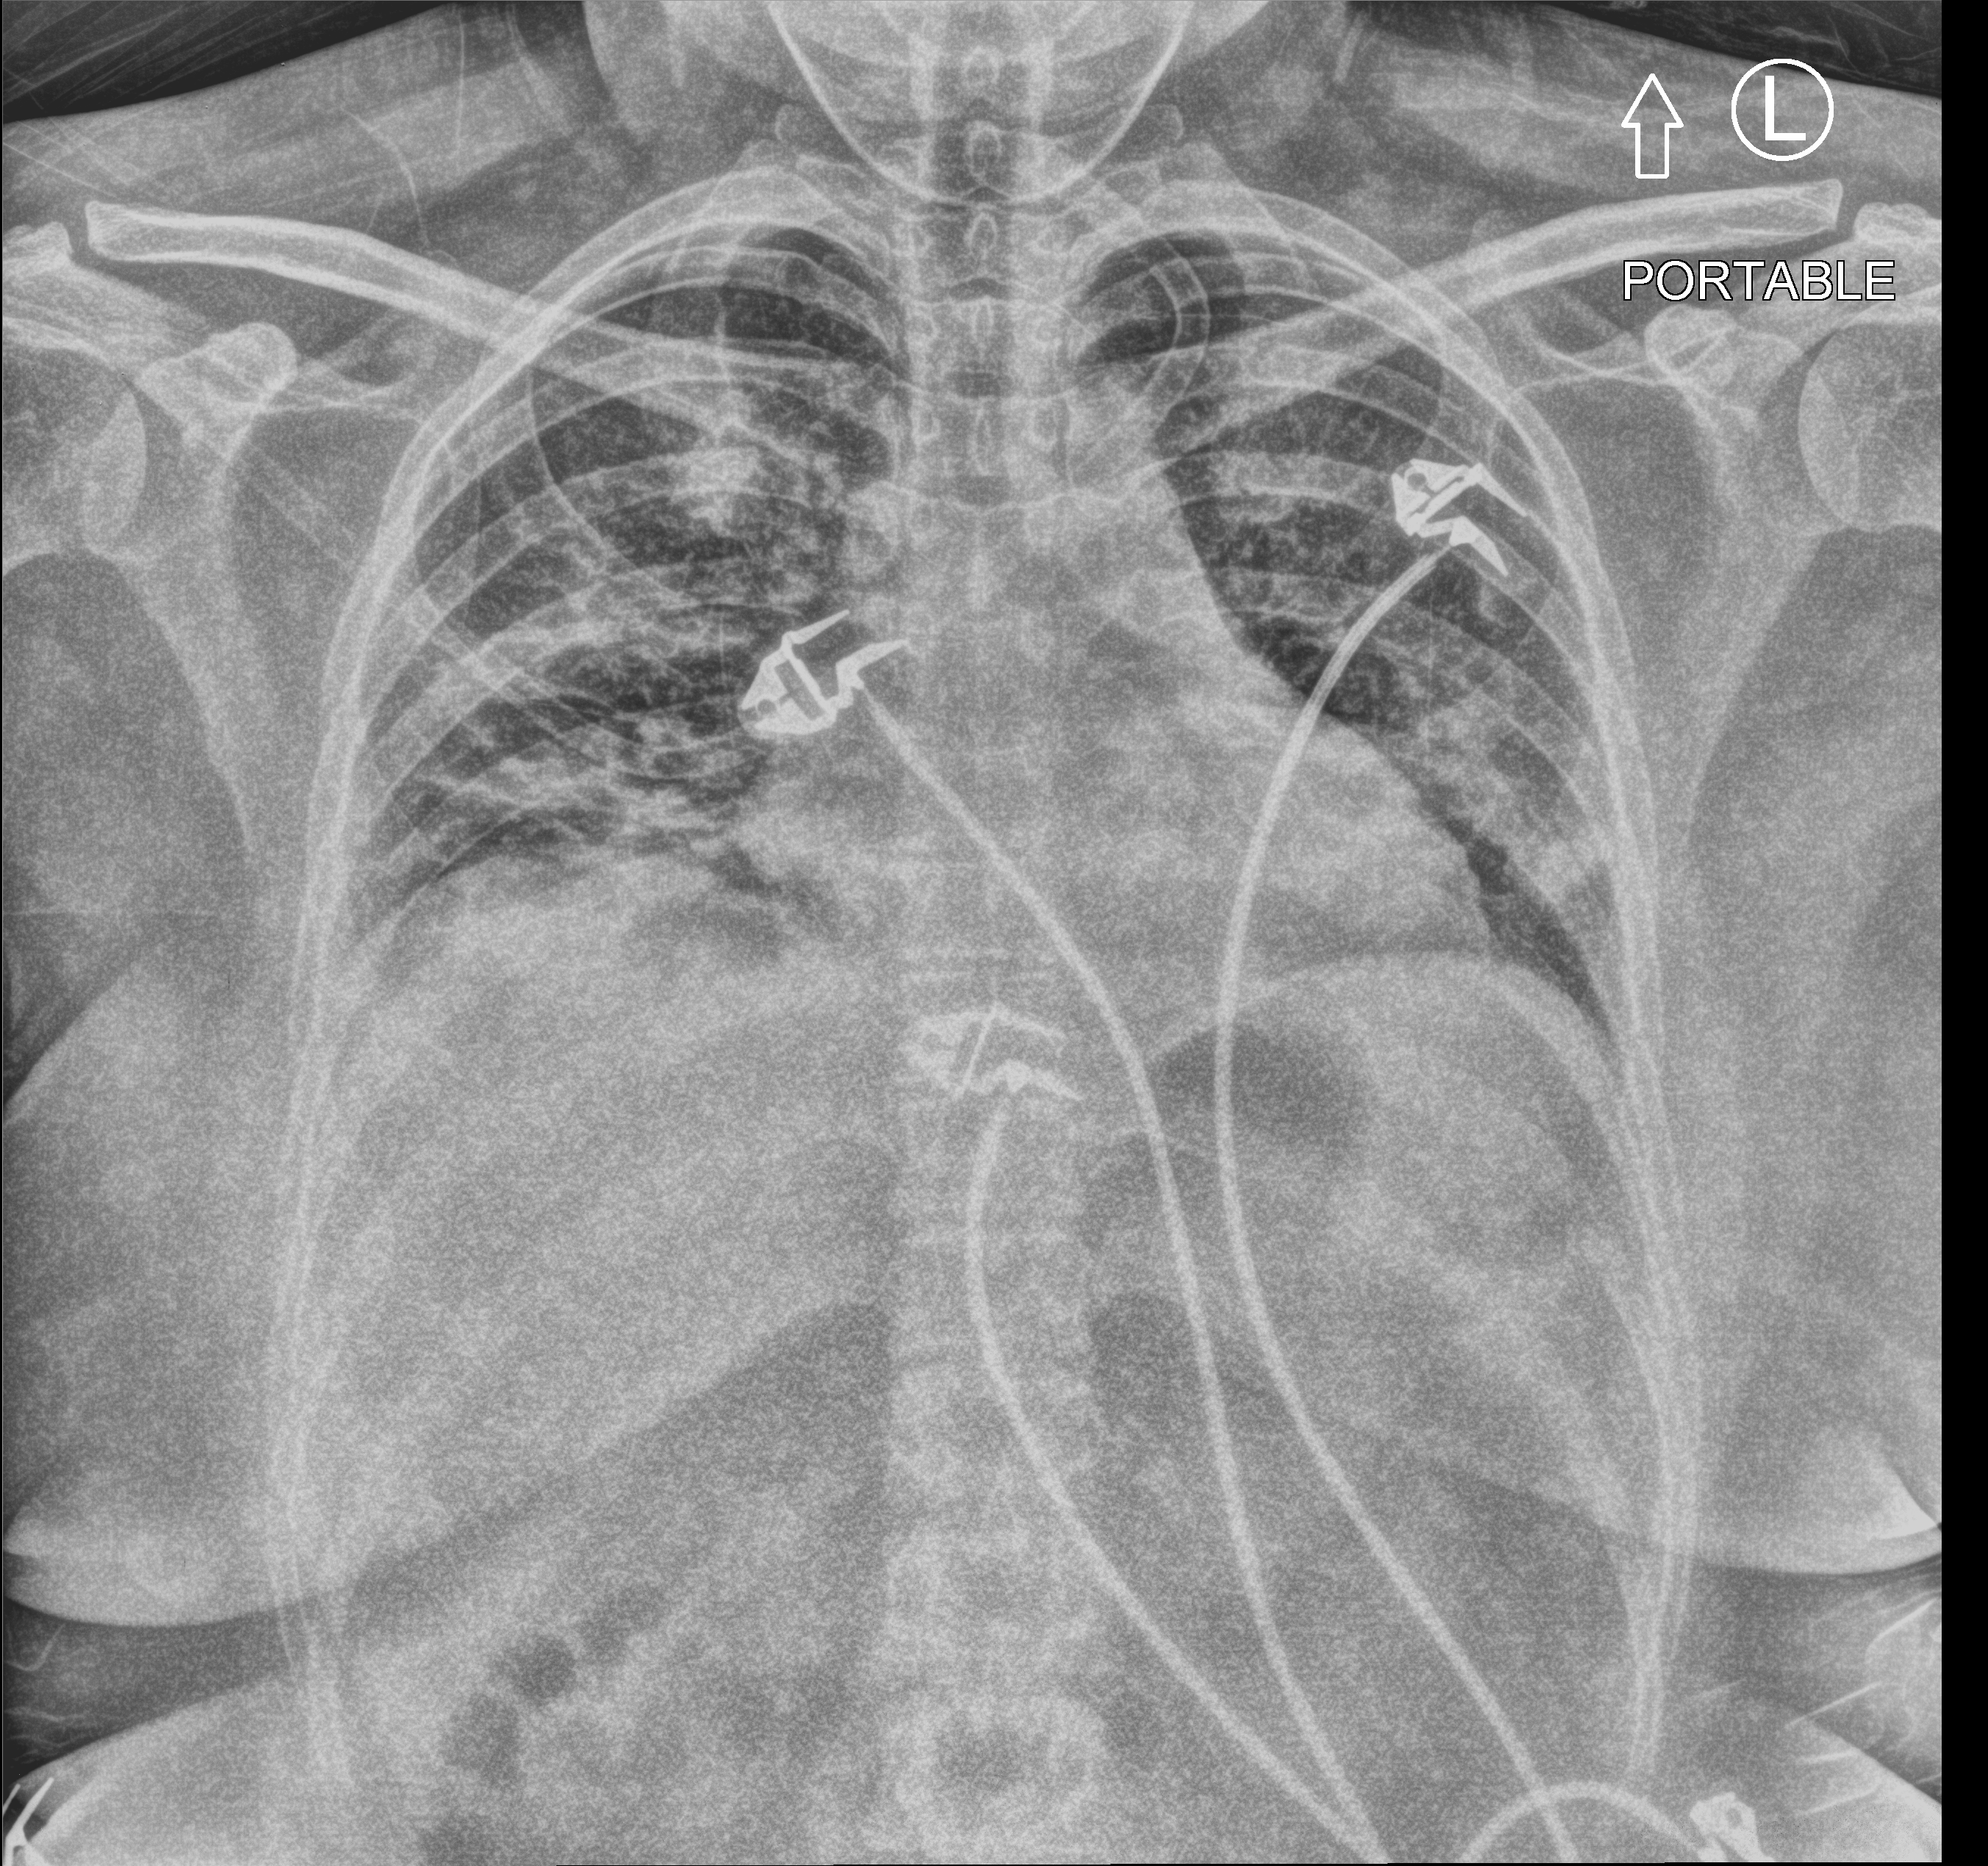
Bedside chest radiograph (computed radiography); anteroposterior (AP) projection. Female patient hospitalised with COVID-19, age 18–59 years.
From the hospital-stay record, not from the radiograph (when in the stay this image was taken is not recorded): smoking status (admission record): never; admitted to intensive care during this hospital stay: no.